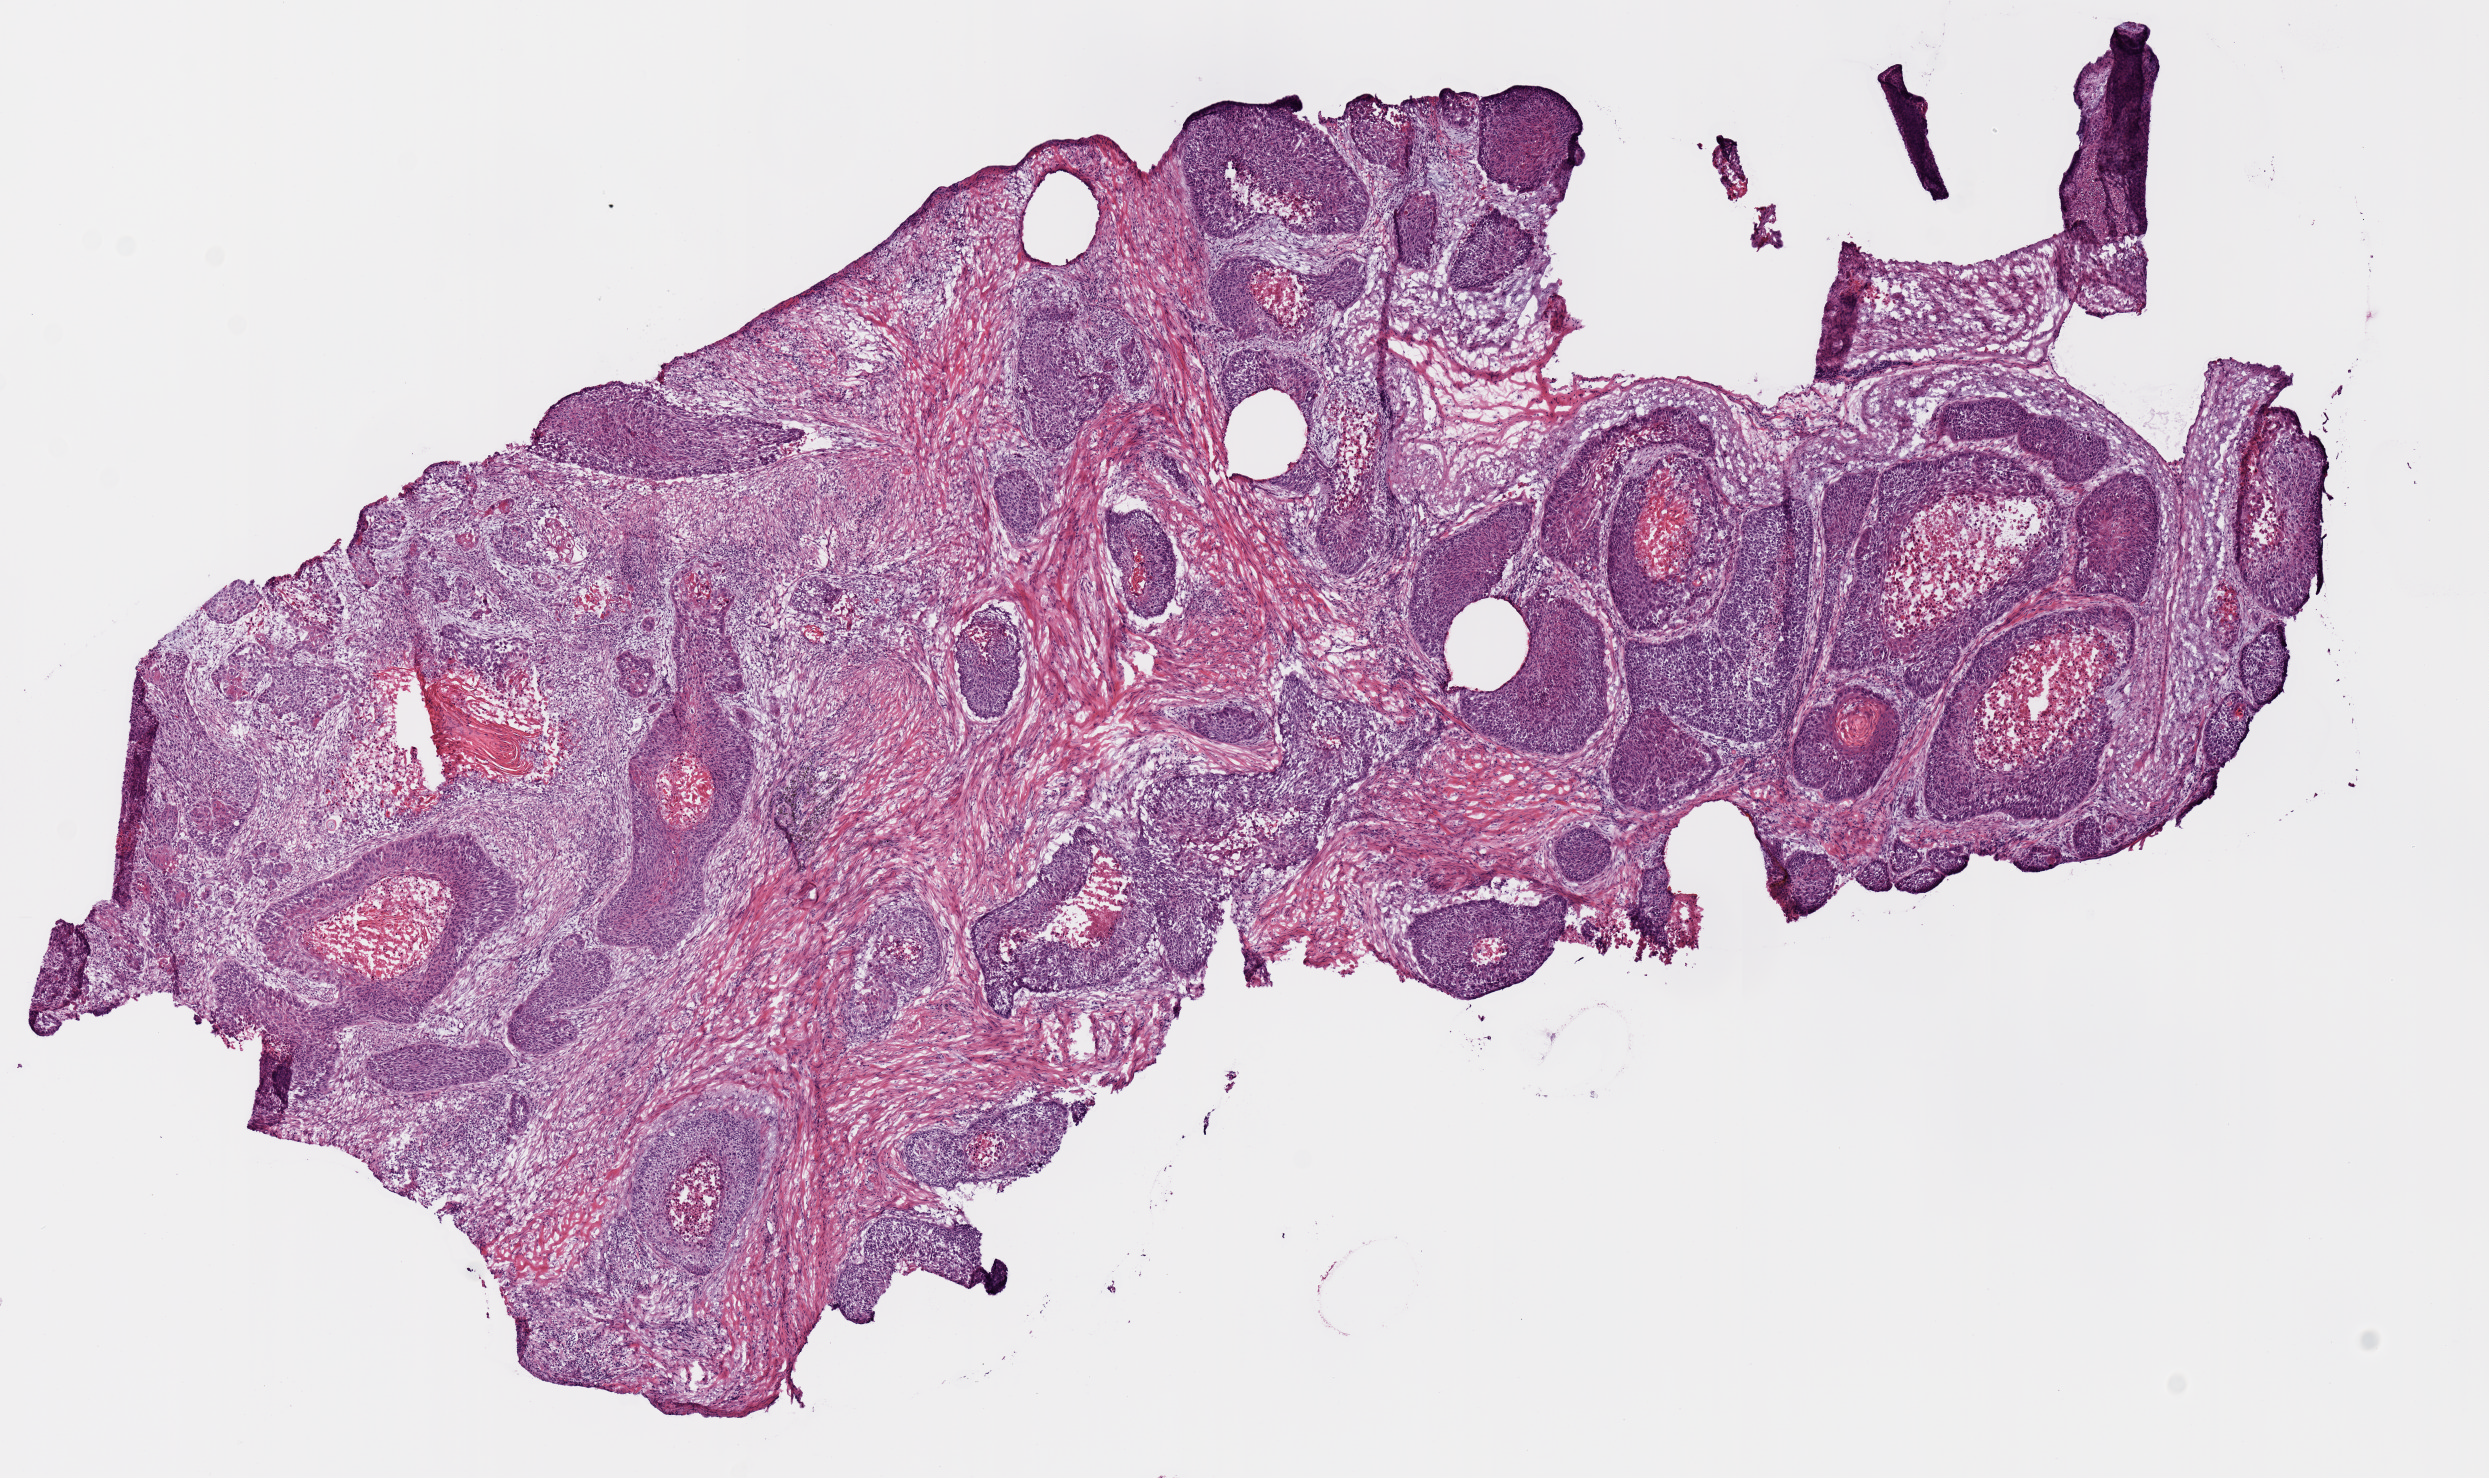
Whole-slide histology image, H&E — whole scanned area (about 9.8 x 5.8 mm, acquisition: 20x scan) shown as a low-resolution overview; frozen section from the top of the tissue portion; lung, primary tumour sample. Patient: male, age at initial diagnosis 83 years.
Pathologic diagnosis: Squamous cell carcinoma, NOS (lower lobe, lung).